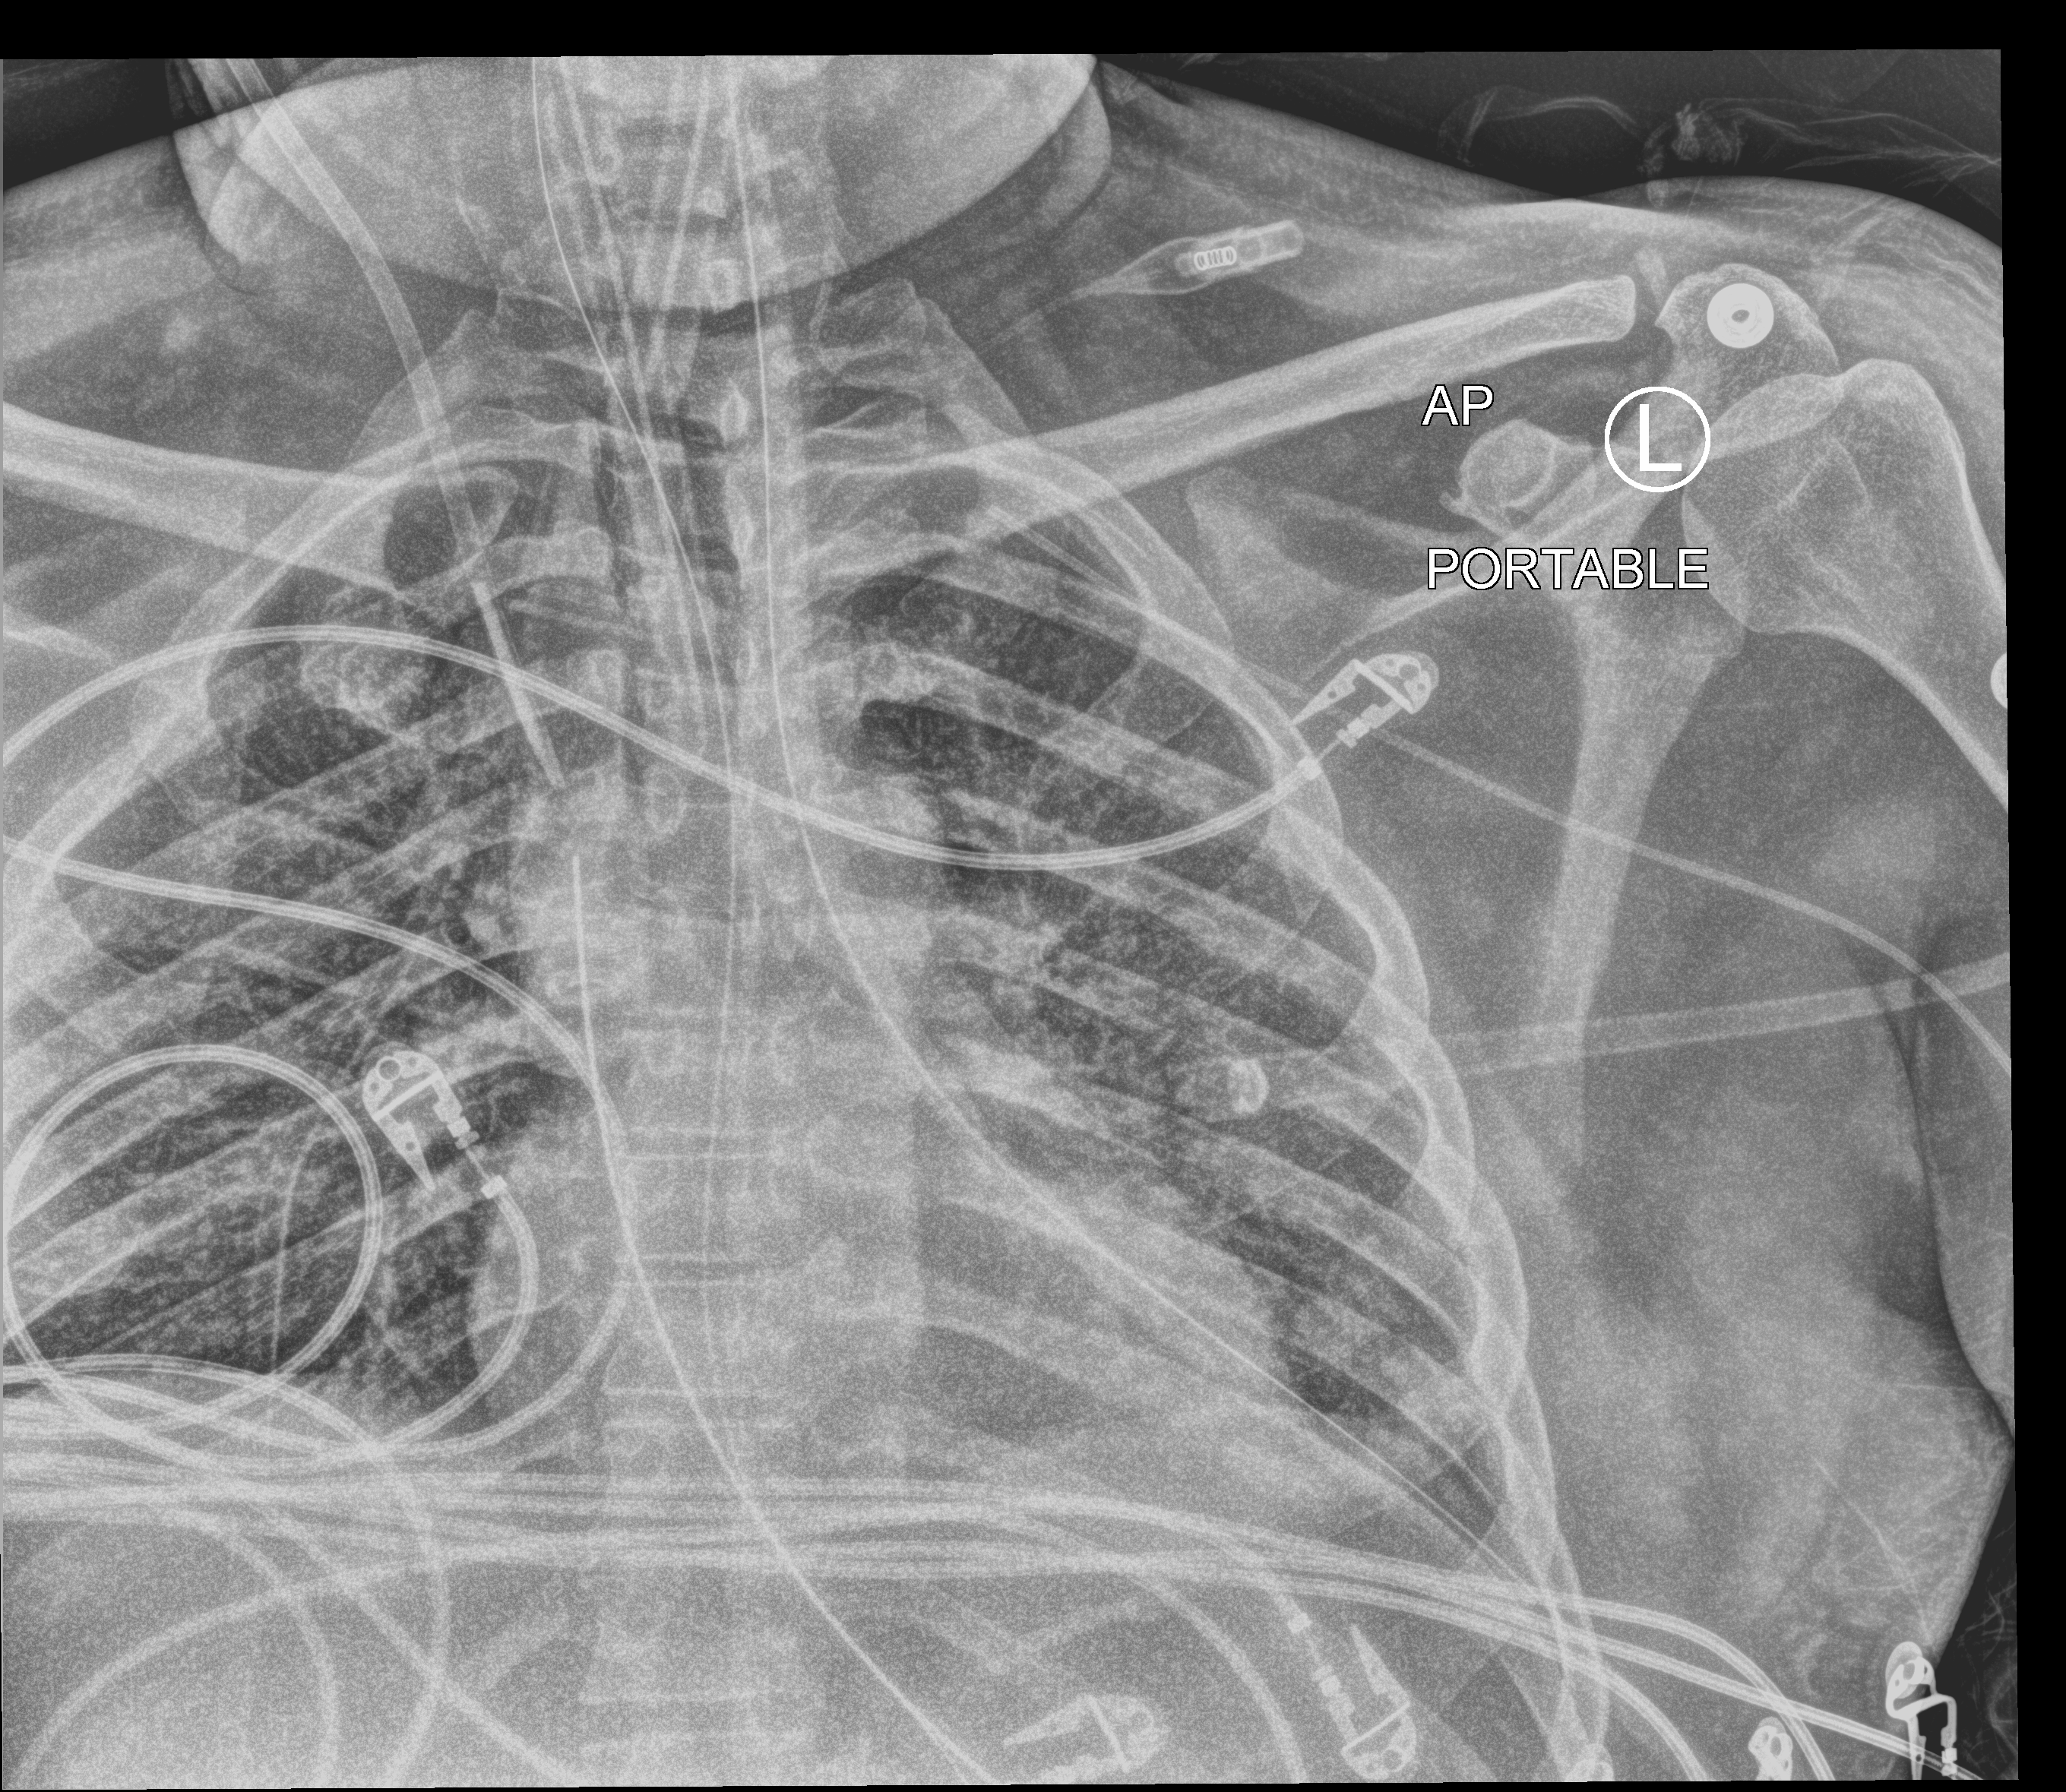
Portable chest radiograph, anteroposterior (AP) projection. Patient hospitalised with COVID-19, aged 18–59 years.
Hospital-stay facts (about this admission, not read from this image; timing relative to this image not recorded): mechanically ventilated during this hospital stay: yes; length of hospital stay: 19 days; smoking status (admission record): never.